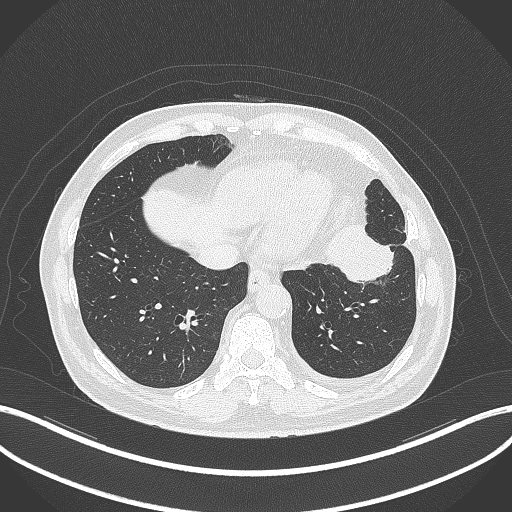
Chest CT, one axial slice. Slice 99 of 230 in the series (ordered by position). Reconstruction kernel B70f. 120 kVp. Lung window (W 1500 / L -600 HU). 1 mm slice thickness. 512 × 512 image matrix, field of view 400 × 400 mm. Patient: male, 68 years. From the clinical record (not read from this slice): clinical TNM (as recorded): T2b N0 M0.
Outlined on this slice (rectangle marked by the reading radiologist):
- lung tumour (recorded histology: squamous cell carcinoma): bounding box <326,218,401,286> (left, top, right, bottom; pixels)